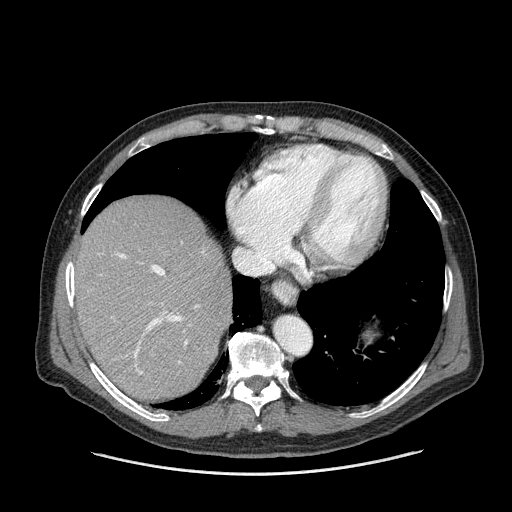
Contrast-enhanced abdominal CT (liver protocol), one axial slice; slice 126 of 180 in the series (ordered by position); reconstruction kernel STANDARD; 120 kVp; one of 2 acquisitions stored at this slice position; soft-tissue window (W 400 / L 40 HU); 2.5 mm slice thickness; 512 × 512 image matrix, field of view 420 × 420 mm. From the clinical record (not read from this slice): diagnosis: hepatocellular carcinoma (patient treated with transarterial chemoembolisation; whether this scan precedes or follows treatment is not stated here); TNM stage (as recorded): Stage-II; Child-Pugh class: A; tumour nodularity: multinodular; tumour size: 2.8 cm.
Annotated regions visible in this slice (semi-automatic segmentation, software-assisted and operator-edited):
- abdominal aorta: bounding box <275,318,311,354> (left, top, right, bottom; pixels)
- liver parenchyma outside the tumour (the mass and vessels are separate outlines, so this box may not span the whole liver): <76,198,230,400>
- liver vessels: <117,253,199,375>